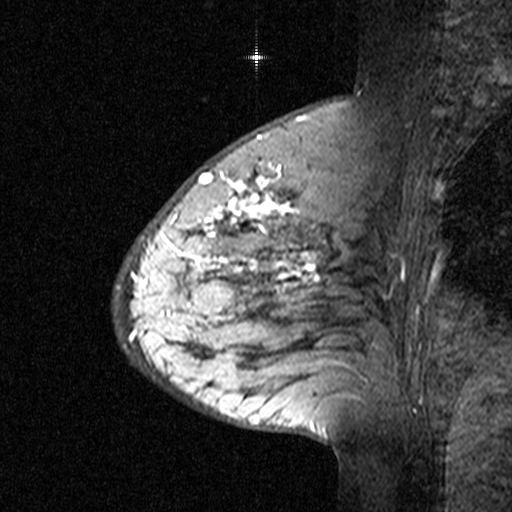
Breast MRI (dynamic contrast-enhanced), one sagittal slice. Slice 13 of 44 in the series (ordered by position). Dynamic contrast-enhanced study with each time point stored as its own series, time point 3 of 4 at this slice position (ordered by acquisition time). 1.5 T. TE 4.5 ms, TR 11 ms. 512 × 512 image matrix, field of view 200 × 200 mm. Patient: female, 65 years. Case-level facts recorded for this patient, not image findings: setting: breast cancer imaged before/during neoadjuvant chemotherapy; receptor status: HER2-positive.
Annotated regions visible in this slice (semi-automatically segmented with operator editing):
- analysis volume of interest (the breast-tissue region the enhancement analysis was run in; not a lesion): bounding box <182,190,353,361> (left, top, right, bottom; pixels)
- tumour enhancement mask (voxels above the 90 % enhancement threshold inside the analysis volume of interest): <182,190,312,287>